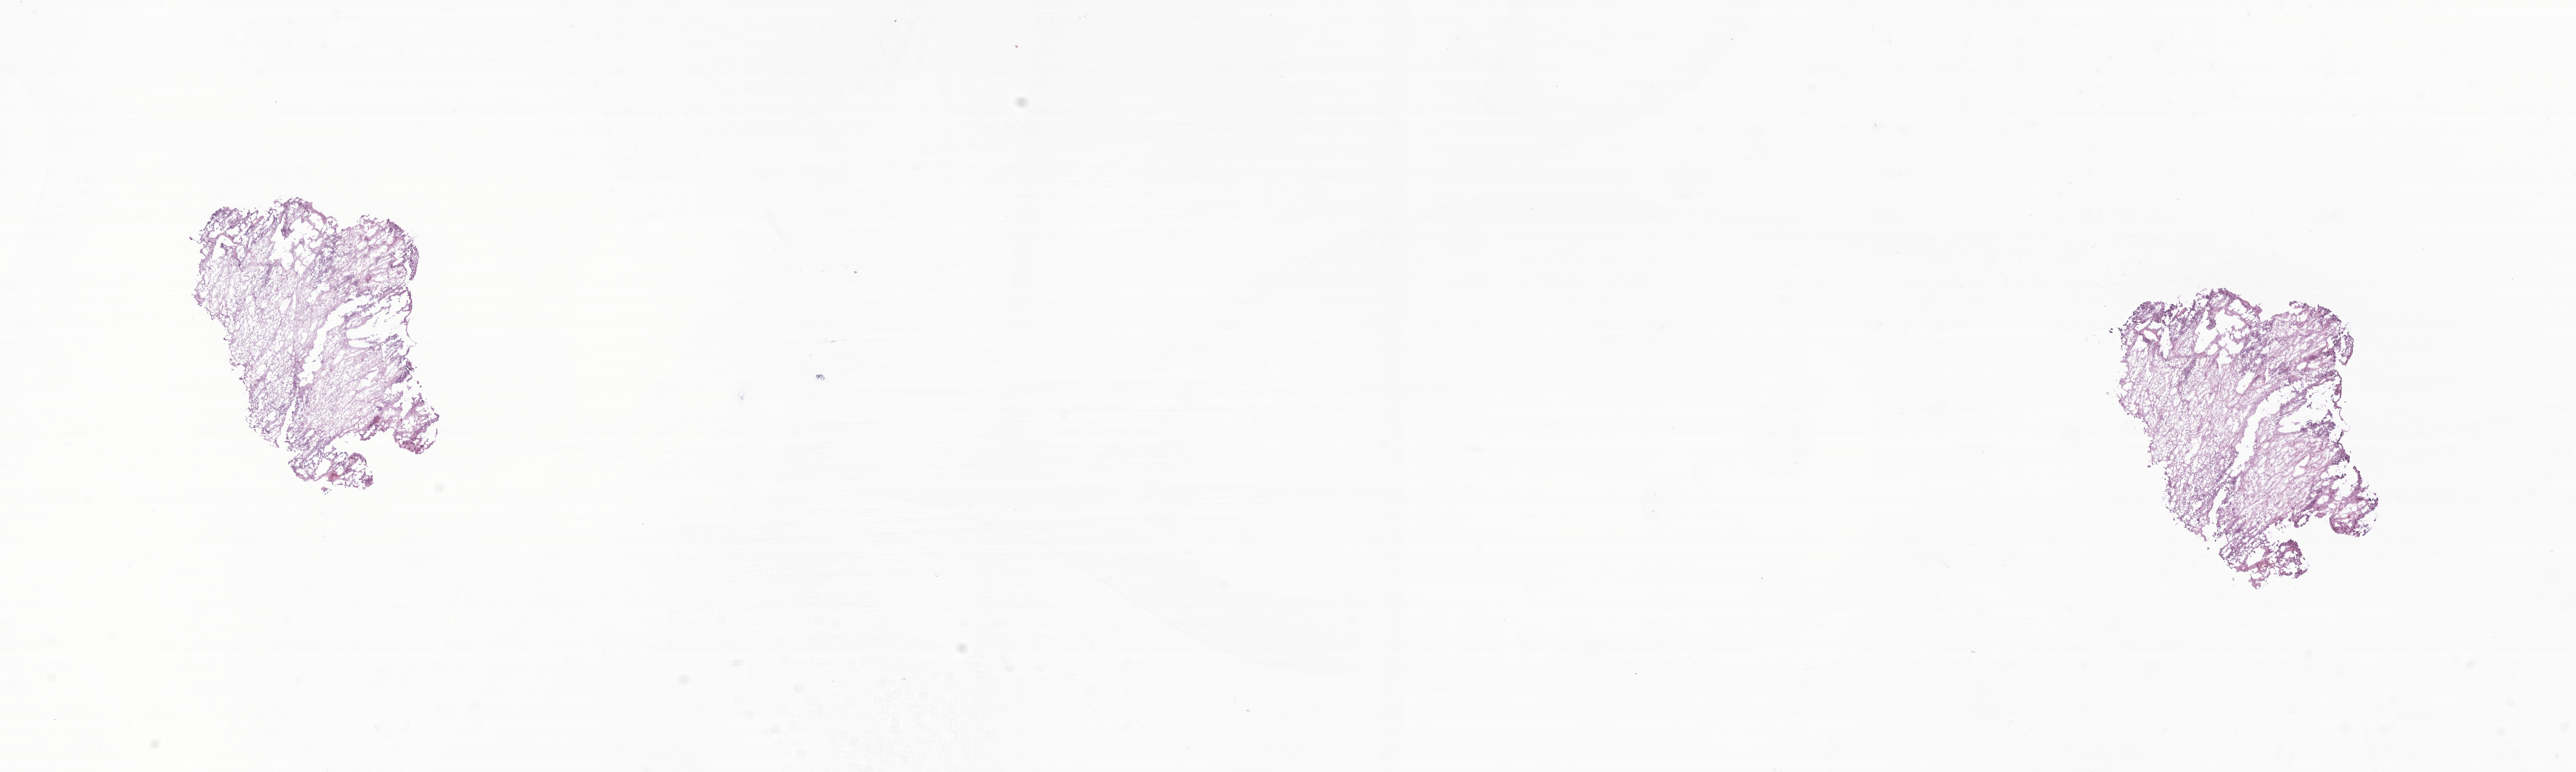
Digitized H&E-stained section of tumor tissue from the cerebral ventricle — a low-resolution overview of the entire scanned area, about 25.6 x 7.7 mm; frozen section (OCT-embedded). Patient male; age 677 days (about 1.9 years).
* recorded diagnosis: Medulloblastoma, NOS